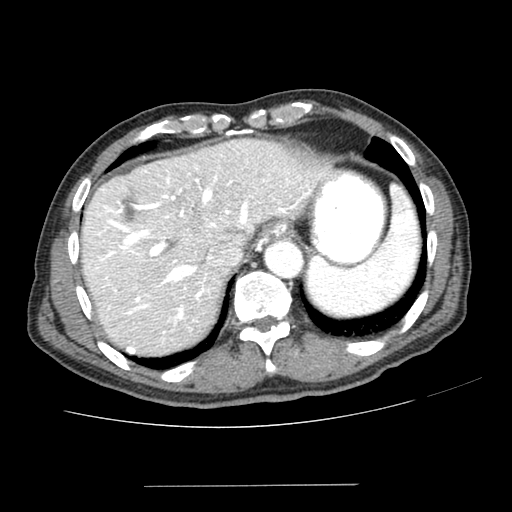
Contrast-enhanced abdominal CT (liver protocol), one axial slice; position 168 of 187 along the scan axis; reconstruction kernel SOFT; 100 kVp; one of 2 acquisitions stored at this slice position; soft-tissue window (W 400 / L 40 HU); 2.5 mm slice thickness; 512 × 512 image matrix, field of view 360 × 360 mm. From the clinical record (not read from this slice): diagnosis: hepatocellular carcinoma (patient treated with transarterial chemoembolisation; whether this scan precedes or follows treatment is not stated here); TNM stage (as recorded): Stage-I; Child-Pugh class: A; tumour differentiation: poorly differentiated; tumour nodularity: uninodular.
Outlined on this slice (semi-automatically segmented with operator editing):
- liver parenchyma outside the tumour (the mass and vessels are separate outlines, so this box may not span the whole liver): bounding box <82,138,332,354> (left, top, right, bottom; pixels)
- liver vessels: <95,155,311,352>